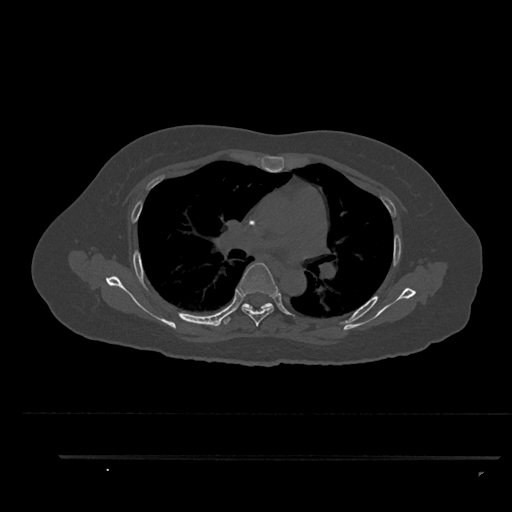
CT including the spine, one axial slice; position 587 of 797 along the scan axis; reconstruction kernel Br40s/3; 120 kVp; bone window (W 1800 / L 400 HU); 0.5 mm slice thickness; 512 × 512 image matrix, field of view 408 × 408 mm. Patient: female, 44 years. Case-level facts recorded for this patient, not image findings: primary cancer: renal.
Annotated regions visible in this slice (semi-automatically segmented with operator editing):
- T5 vertebra: bounding box <239,262,278,327> (left, top, right, bottom; pixels)
- T6 vertebra: <225,303,273,324>